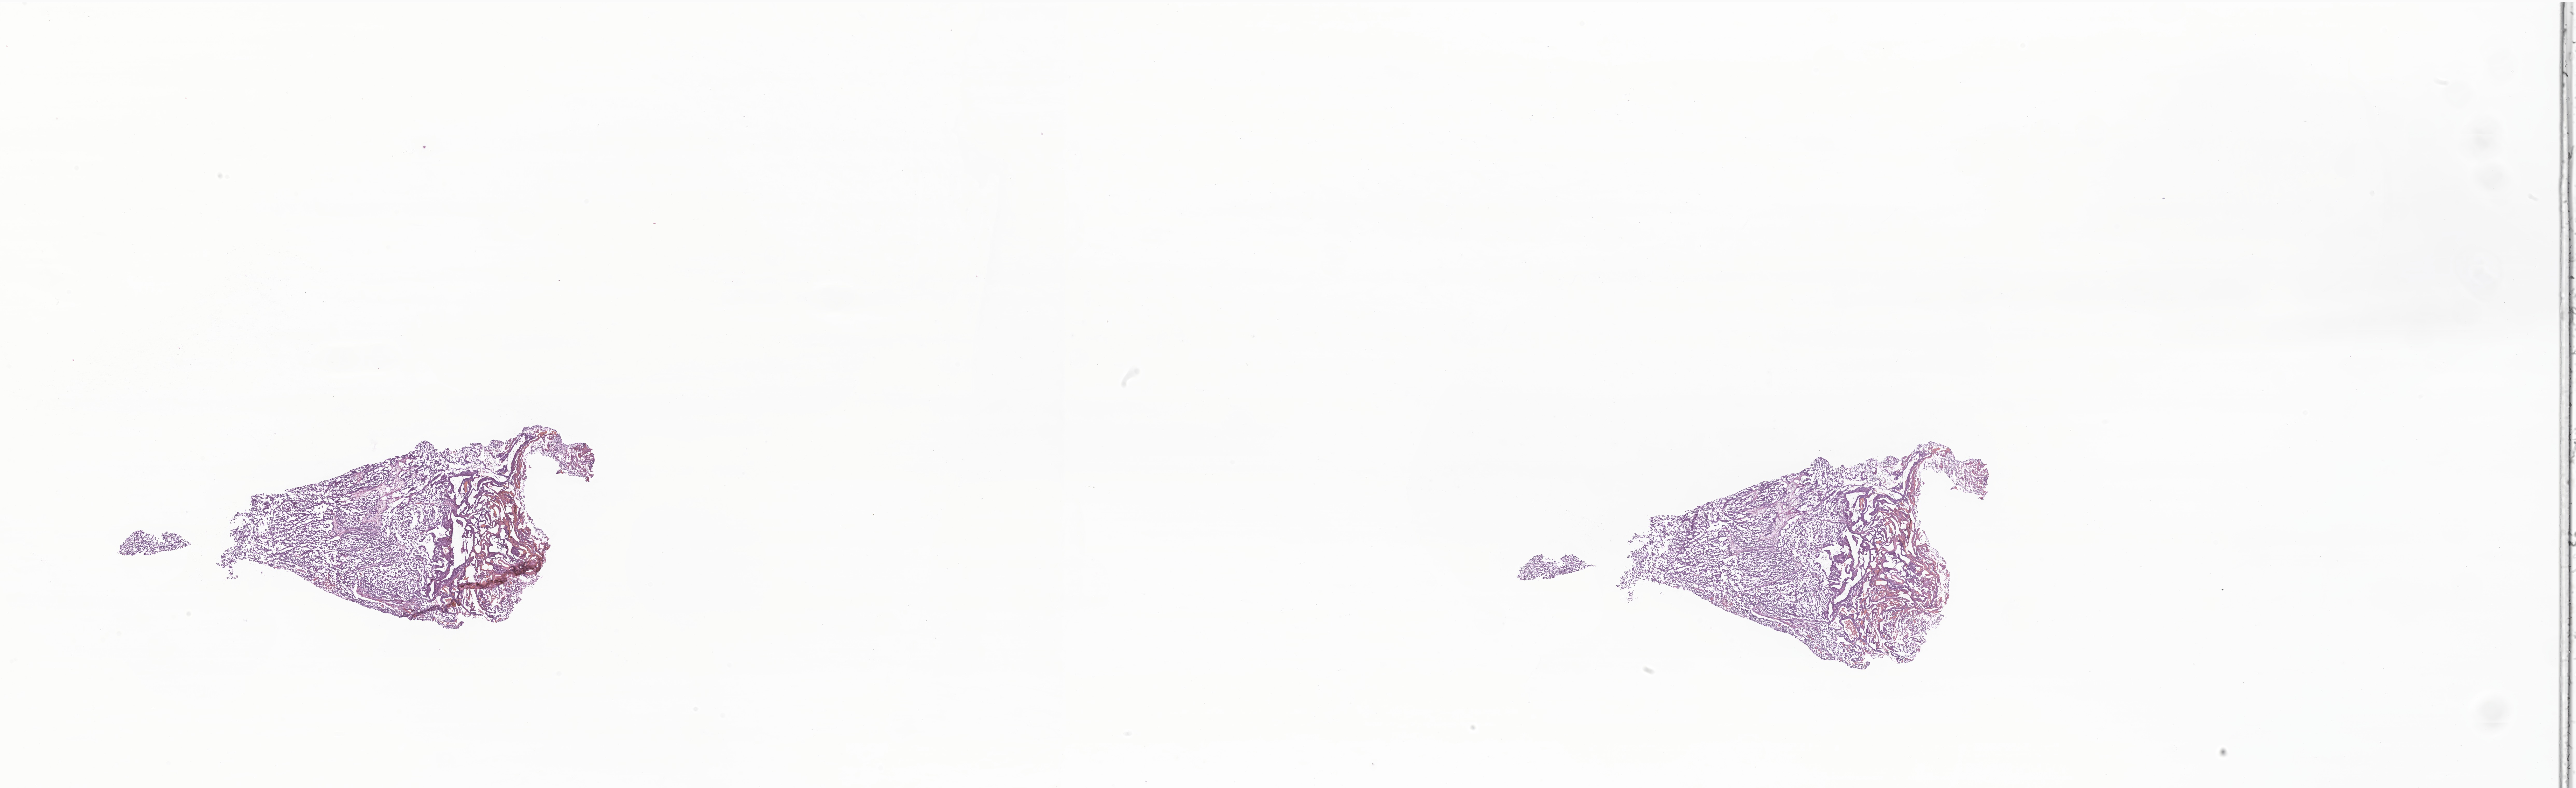
Whole-slide image, haematoxylin and eosin stain of tumor tissue from the brain, a low-resolution overview of the entire scanned area, about 41.6 x 12.7 mm; frozen section (OCT-embedded). Patient male; age 200 months (16 years 8 months).
* diagnosis (ICD-O-3 morphology term): Medulloblastoma, NOS